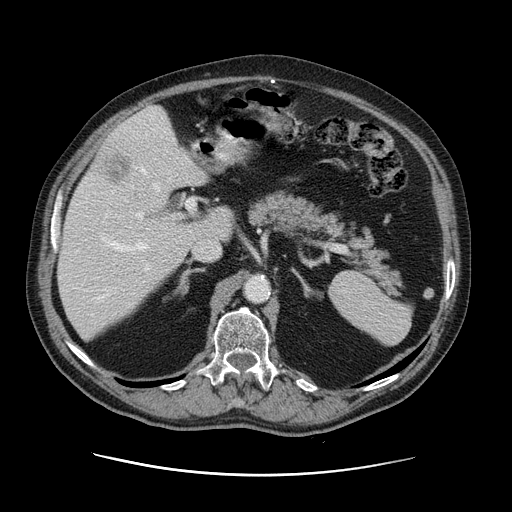
Contrast-enhanced abdominal CT, one axial slice. Slice 76 of 141 in the series (ordered by position). Soft-tissue window (W 400 / L 40 HU). 512 × 512 image matrix. Male patient, age 72 years. Case-level facts recorded for this patient, not image findings: diagnosis: colorectal cancer liver metastases, imaged before liver resection; multiple liver metastases: yes; largest metastasis: 5.4 cm.
Annotated regions visible in this slice (expert manual segmentation):
- hepatic veins: bounding box <97,134,171,299> (left, top, right, bottom; pixels)
- liver: <58,107,234,339>
- planned liver remnant (the part of the liver to remain after resection): <58,166,234,339>
- portal vein (with intrahepatic branches): <101,198,195,271>
- liver metastasis: <106,155,131,184>